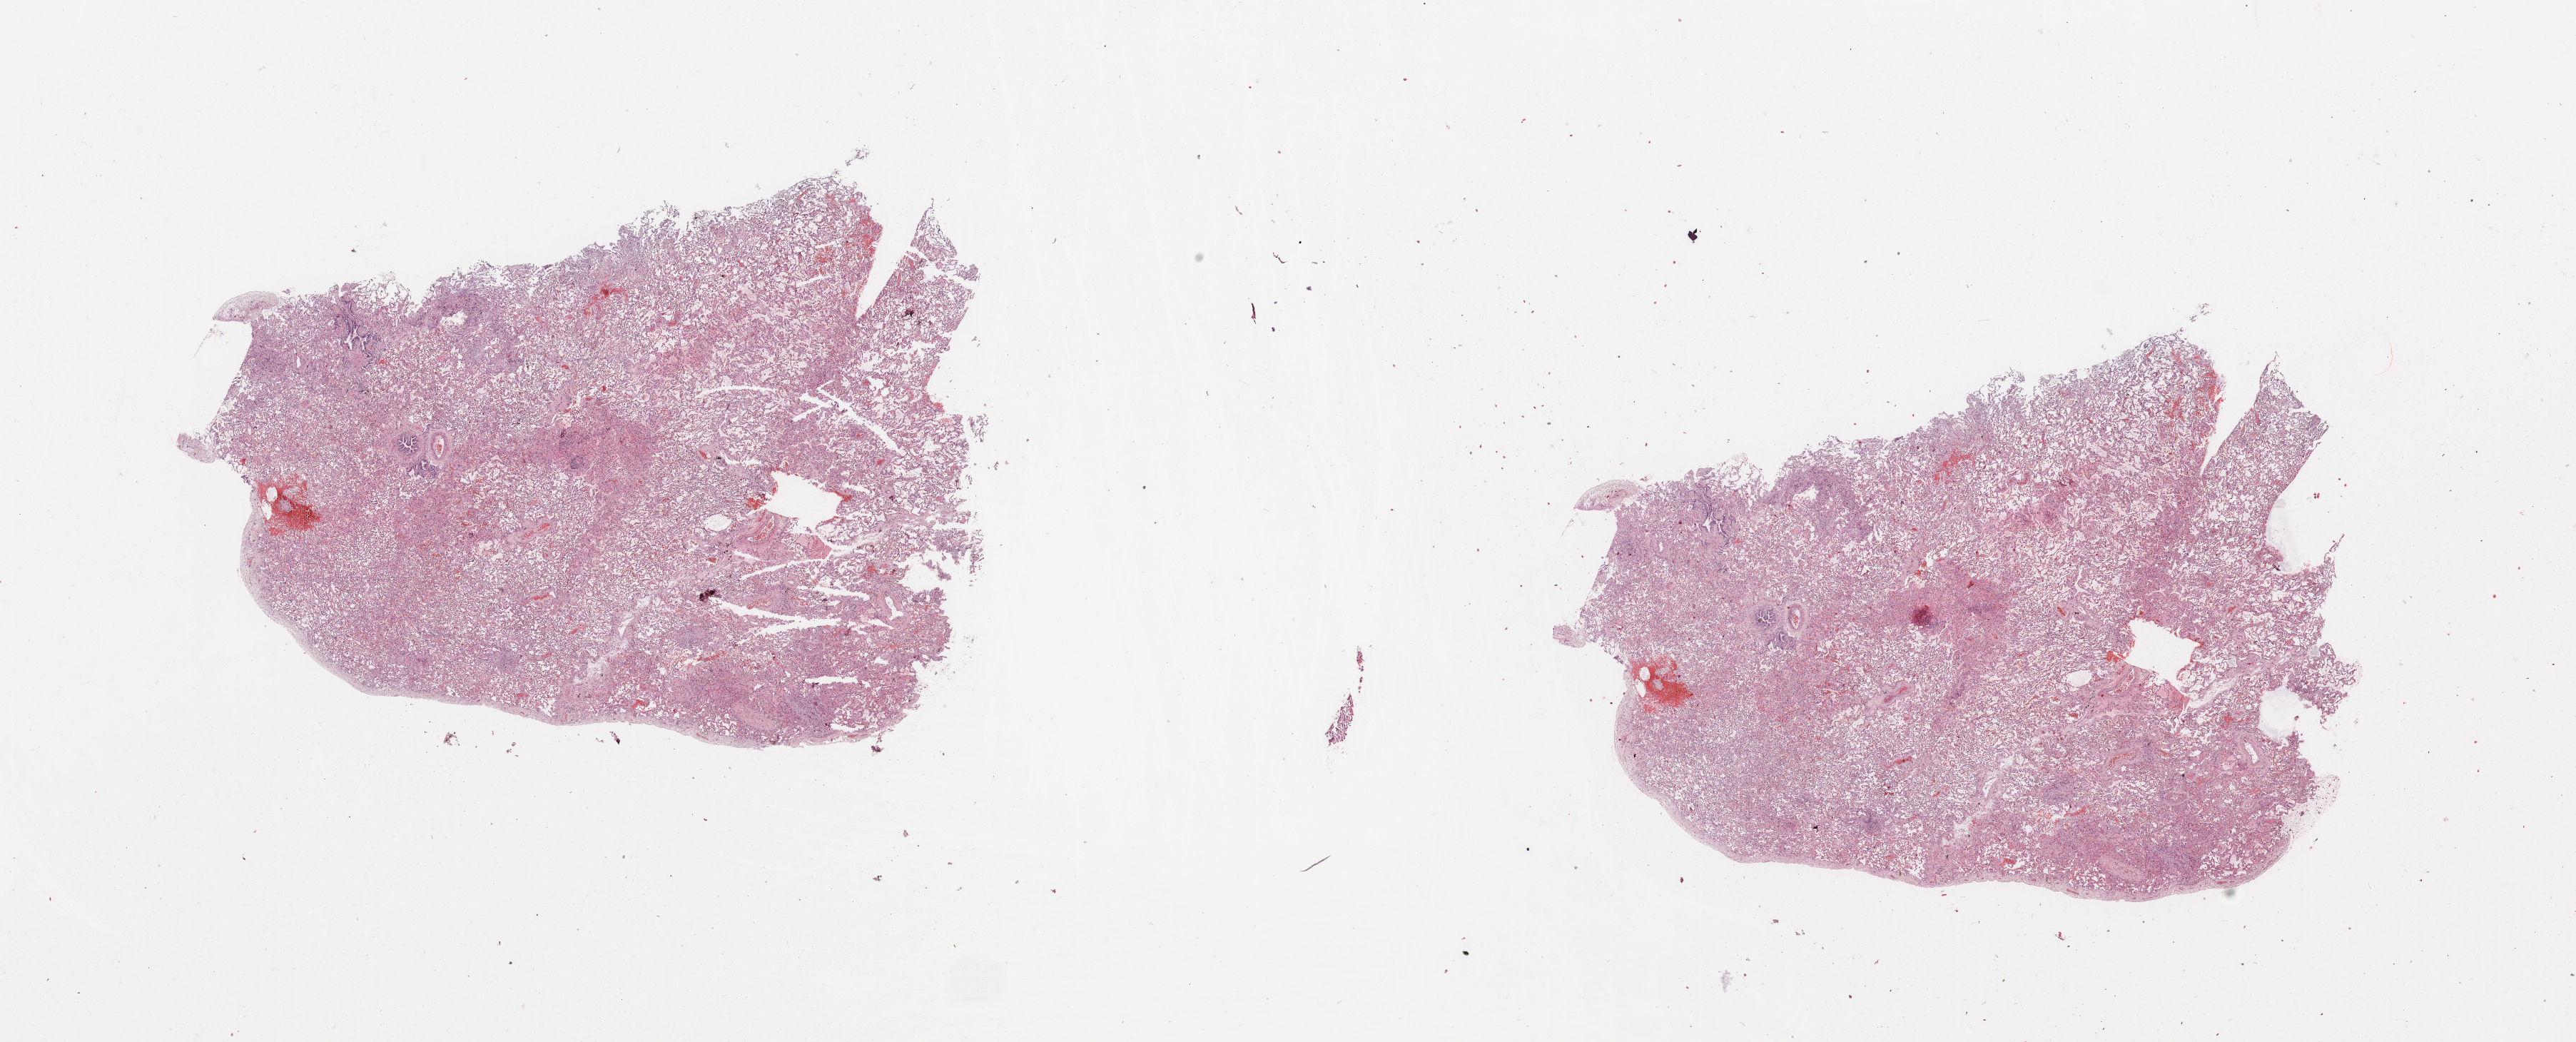
Digitized Hematoxylin and eosin (H&E) stained tissue section (whole slide), shown as a low-resolution overview of the whole scanned area (about 28.5 x 11.5 mm); lung, tissue type not recorded.
- patient diagnosis (cohort enrolment): lung adenocarcinoma (lung)